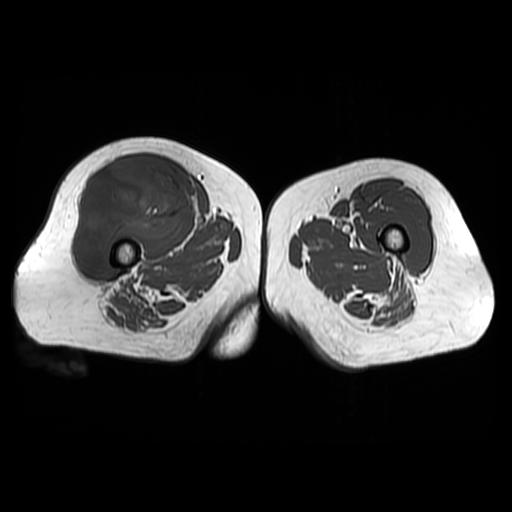
MRI of an extremity soft-tissue mass, one axial slice; position 31 of 48 along the scan axis; 6 mm slice thickness; 512 × 512 image matrix, field of view 440 × 440 mm. Female patient. Case-level facts recorded for this patient, not image findings: histological type: pleiomorphic undifferentiated sarcoma; grade: high; site of the primary tumour: right quadricep.
Outlined on this slice (outlined manually by an expert reader):
- gross tumour volume including surrounding oedema: box from (x=73, y=161) to (x=191, y=269) px
- gross tumour volume (mass): (x=73, y=161)–(x=191, y=269)